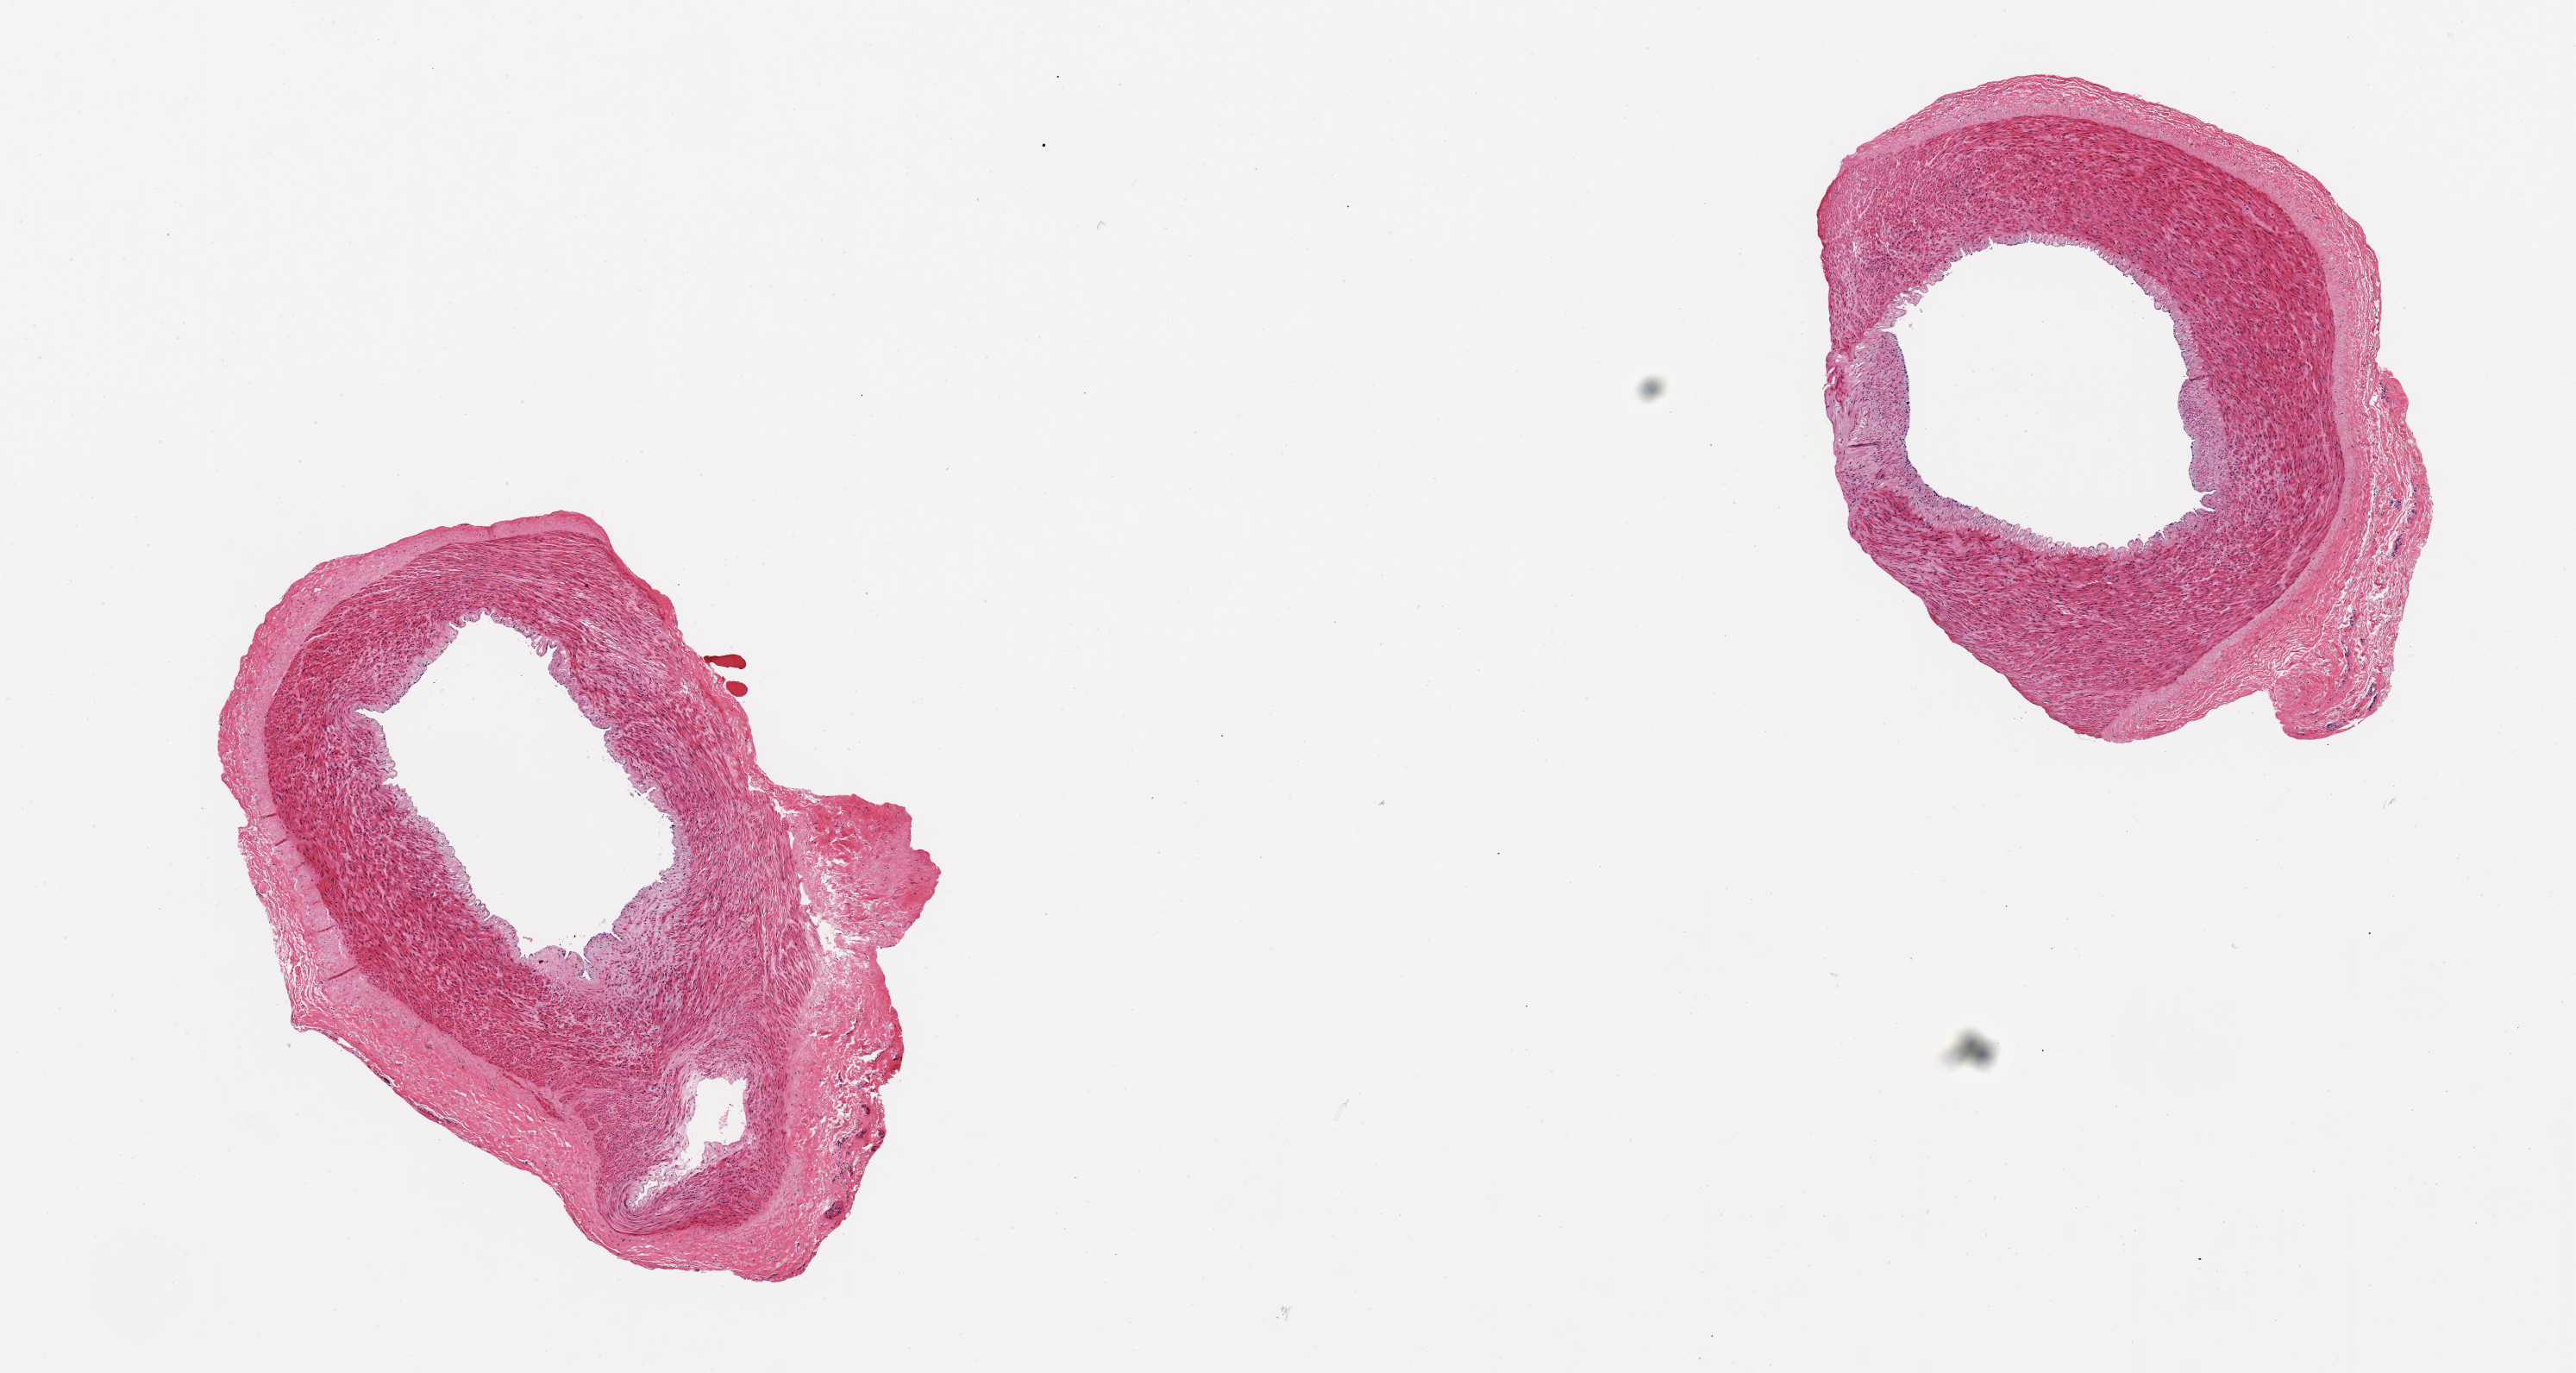
Whole-slide image, hematoxylin and eosin (H&E) stain, shown as a low-resolution overview of the whole scanned area (about 11.8 x 6.3 mm, from a 20x scan); PAXgene-fixed paraffin-embedded (PFPE) section; sampled site (target tissue): tibial artery; tissue donor sample. Donor sex: male.
Reviewer comment on this tissue sample: 2 pieces; focal intimal thickening.